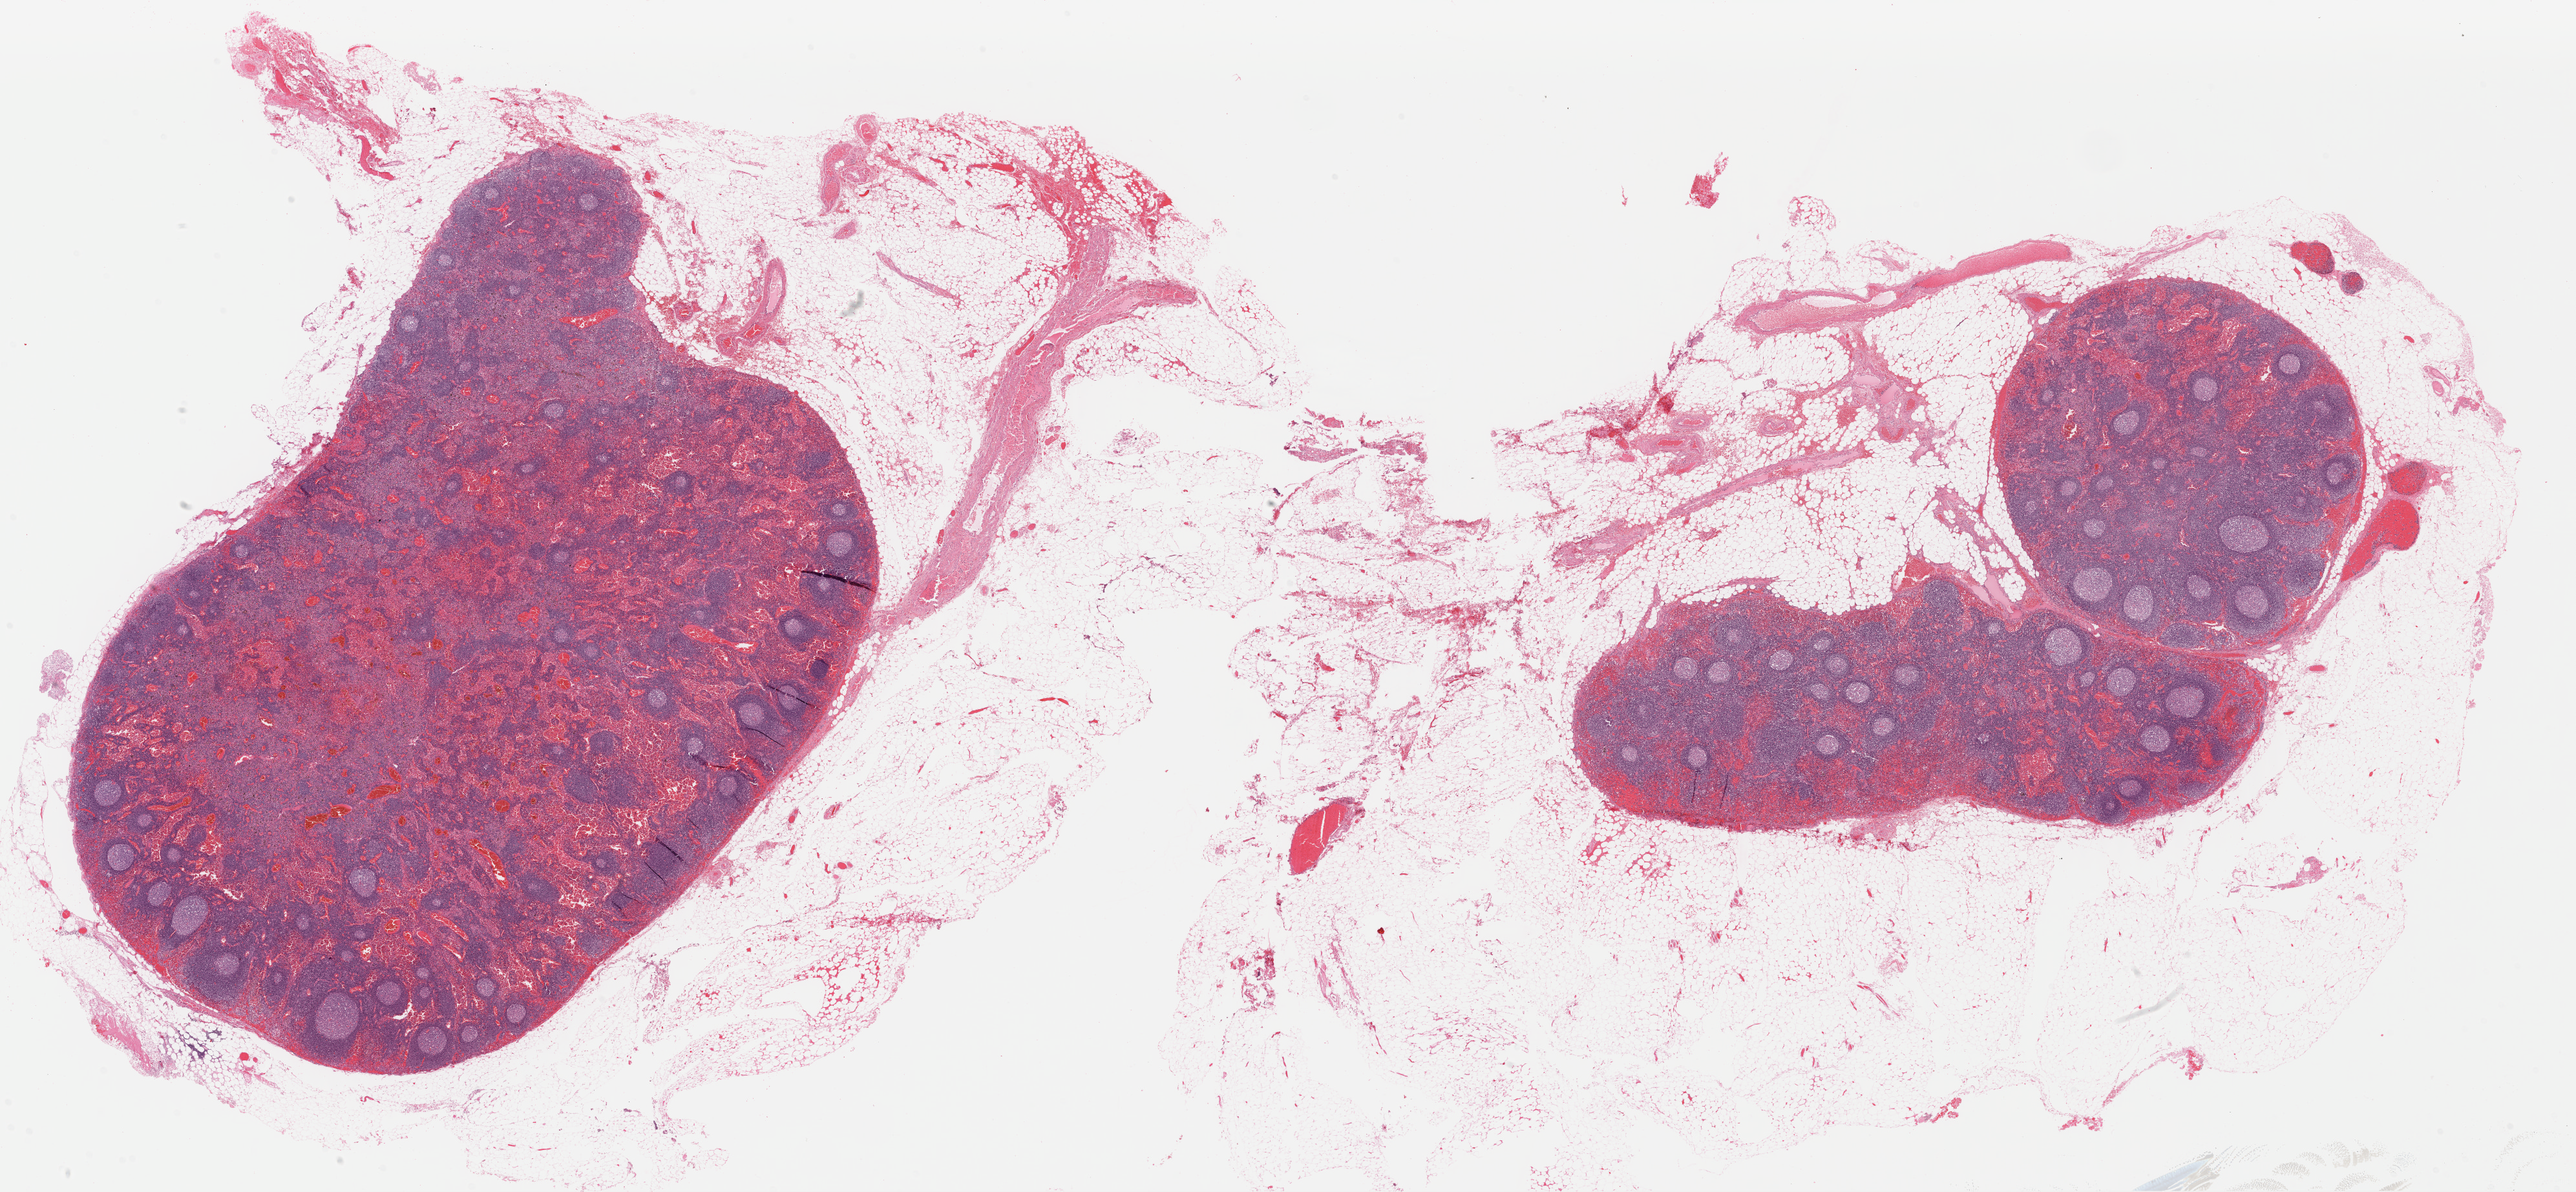
Digitized H&E-stained tissue section (whole slide), low-resolution overview of the scanned area, about 31.3 x 14.5 mm (from a 40x scan), formalin-fixed paraffin-embedded (FFPE) diagnostic section, lung, primary tumour sample. Patient: male, age at initial diagnosis 64 years.
AJCC pathologic stage: IIIB. Histologic diagnosis: Papillary squamous cell carcinoma (upper lobe, lung). Laterality: left.